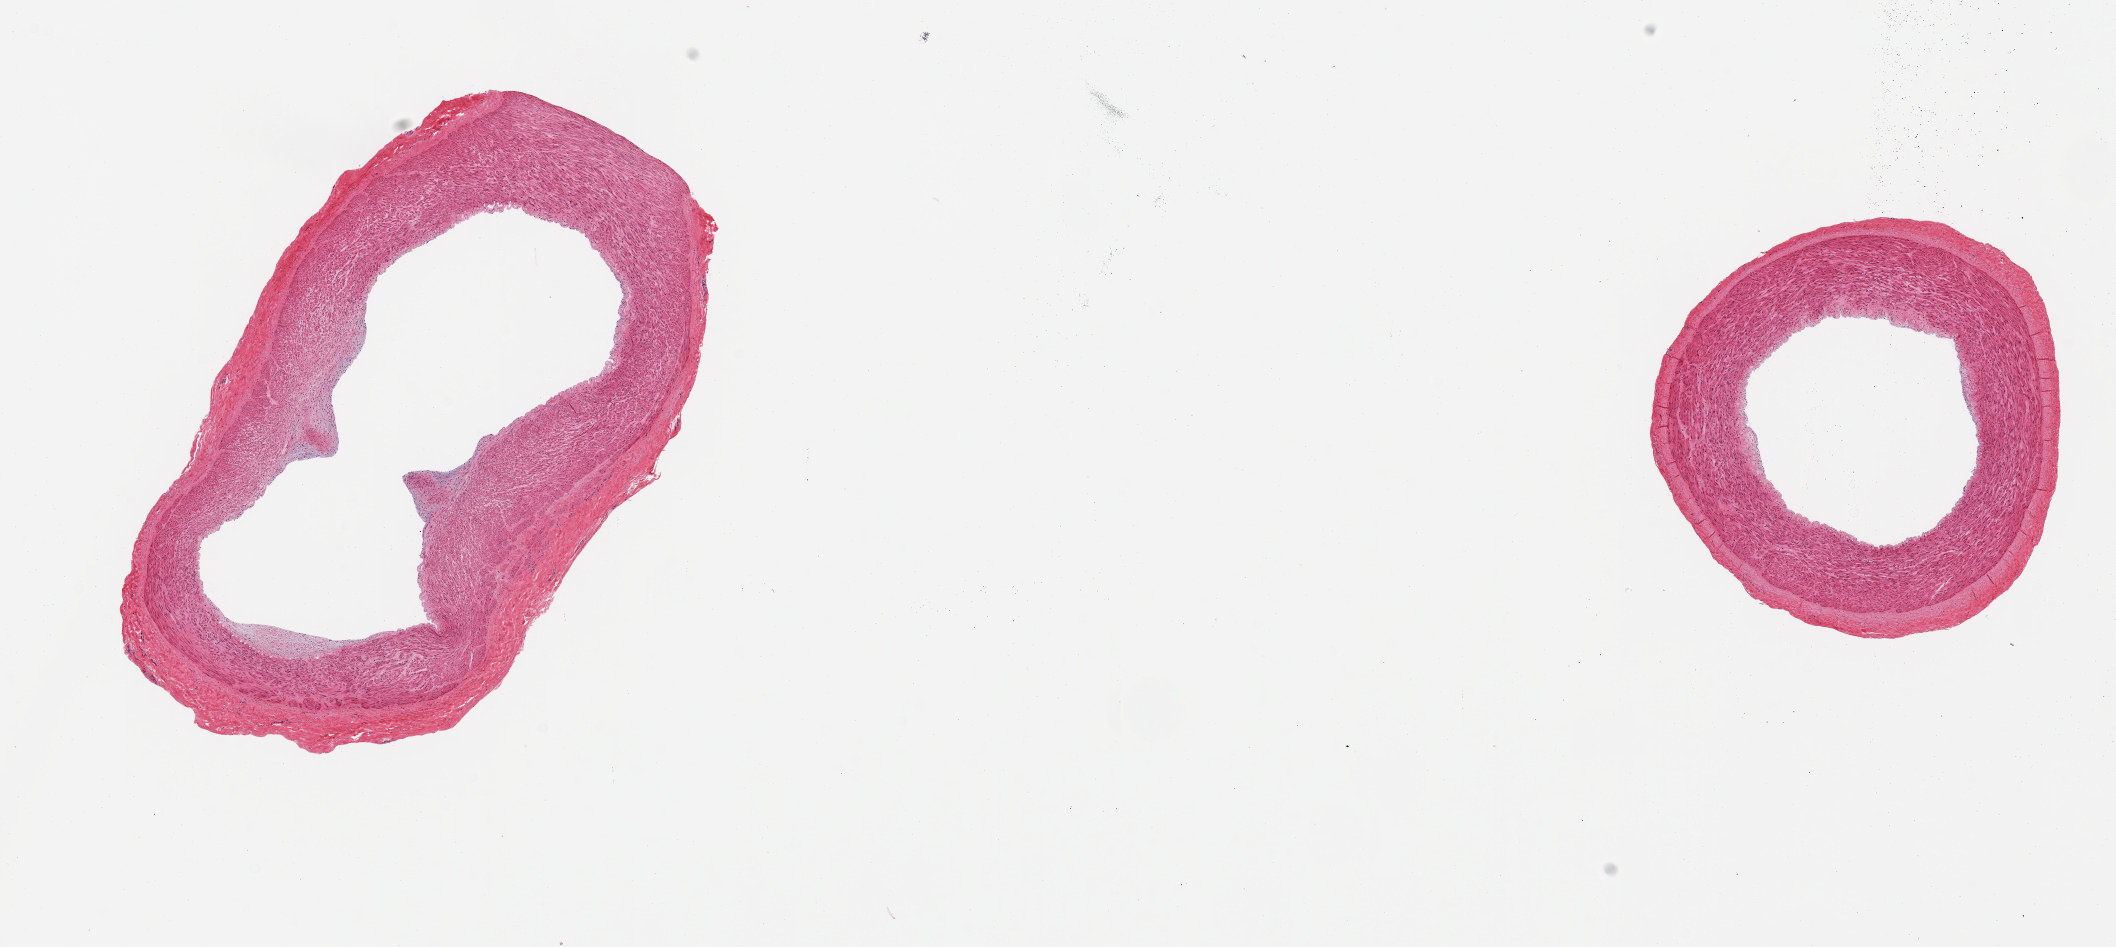
Digitized haematoxylin and eosin-stained section — a low-resolution overview of the entire scanned area, about 16.7 x 7.5 mm (from a 20x scan); PAXgene-fixed paraffin-embedded (PFPE) section; section of tibial artery (target tissue); donor tissue sample. Donor sex: male.
- pathologist's review note for this sample: 2 pieces; well trimmed, widely patent with focal intimal thickening